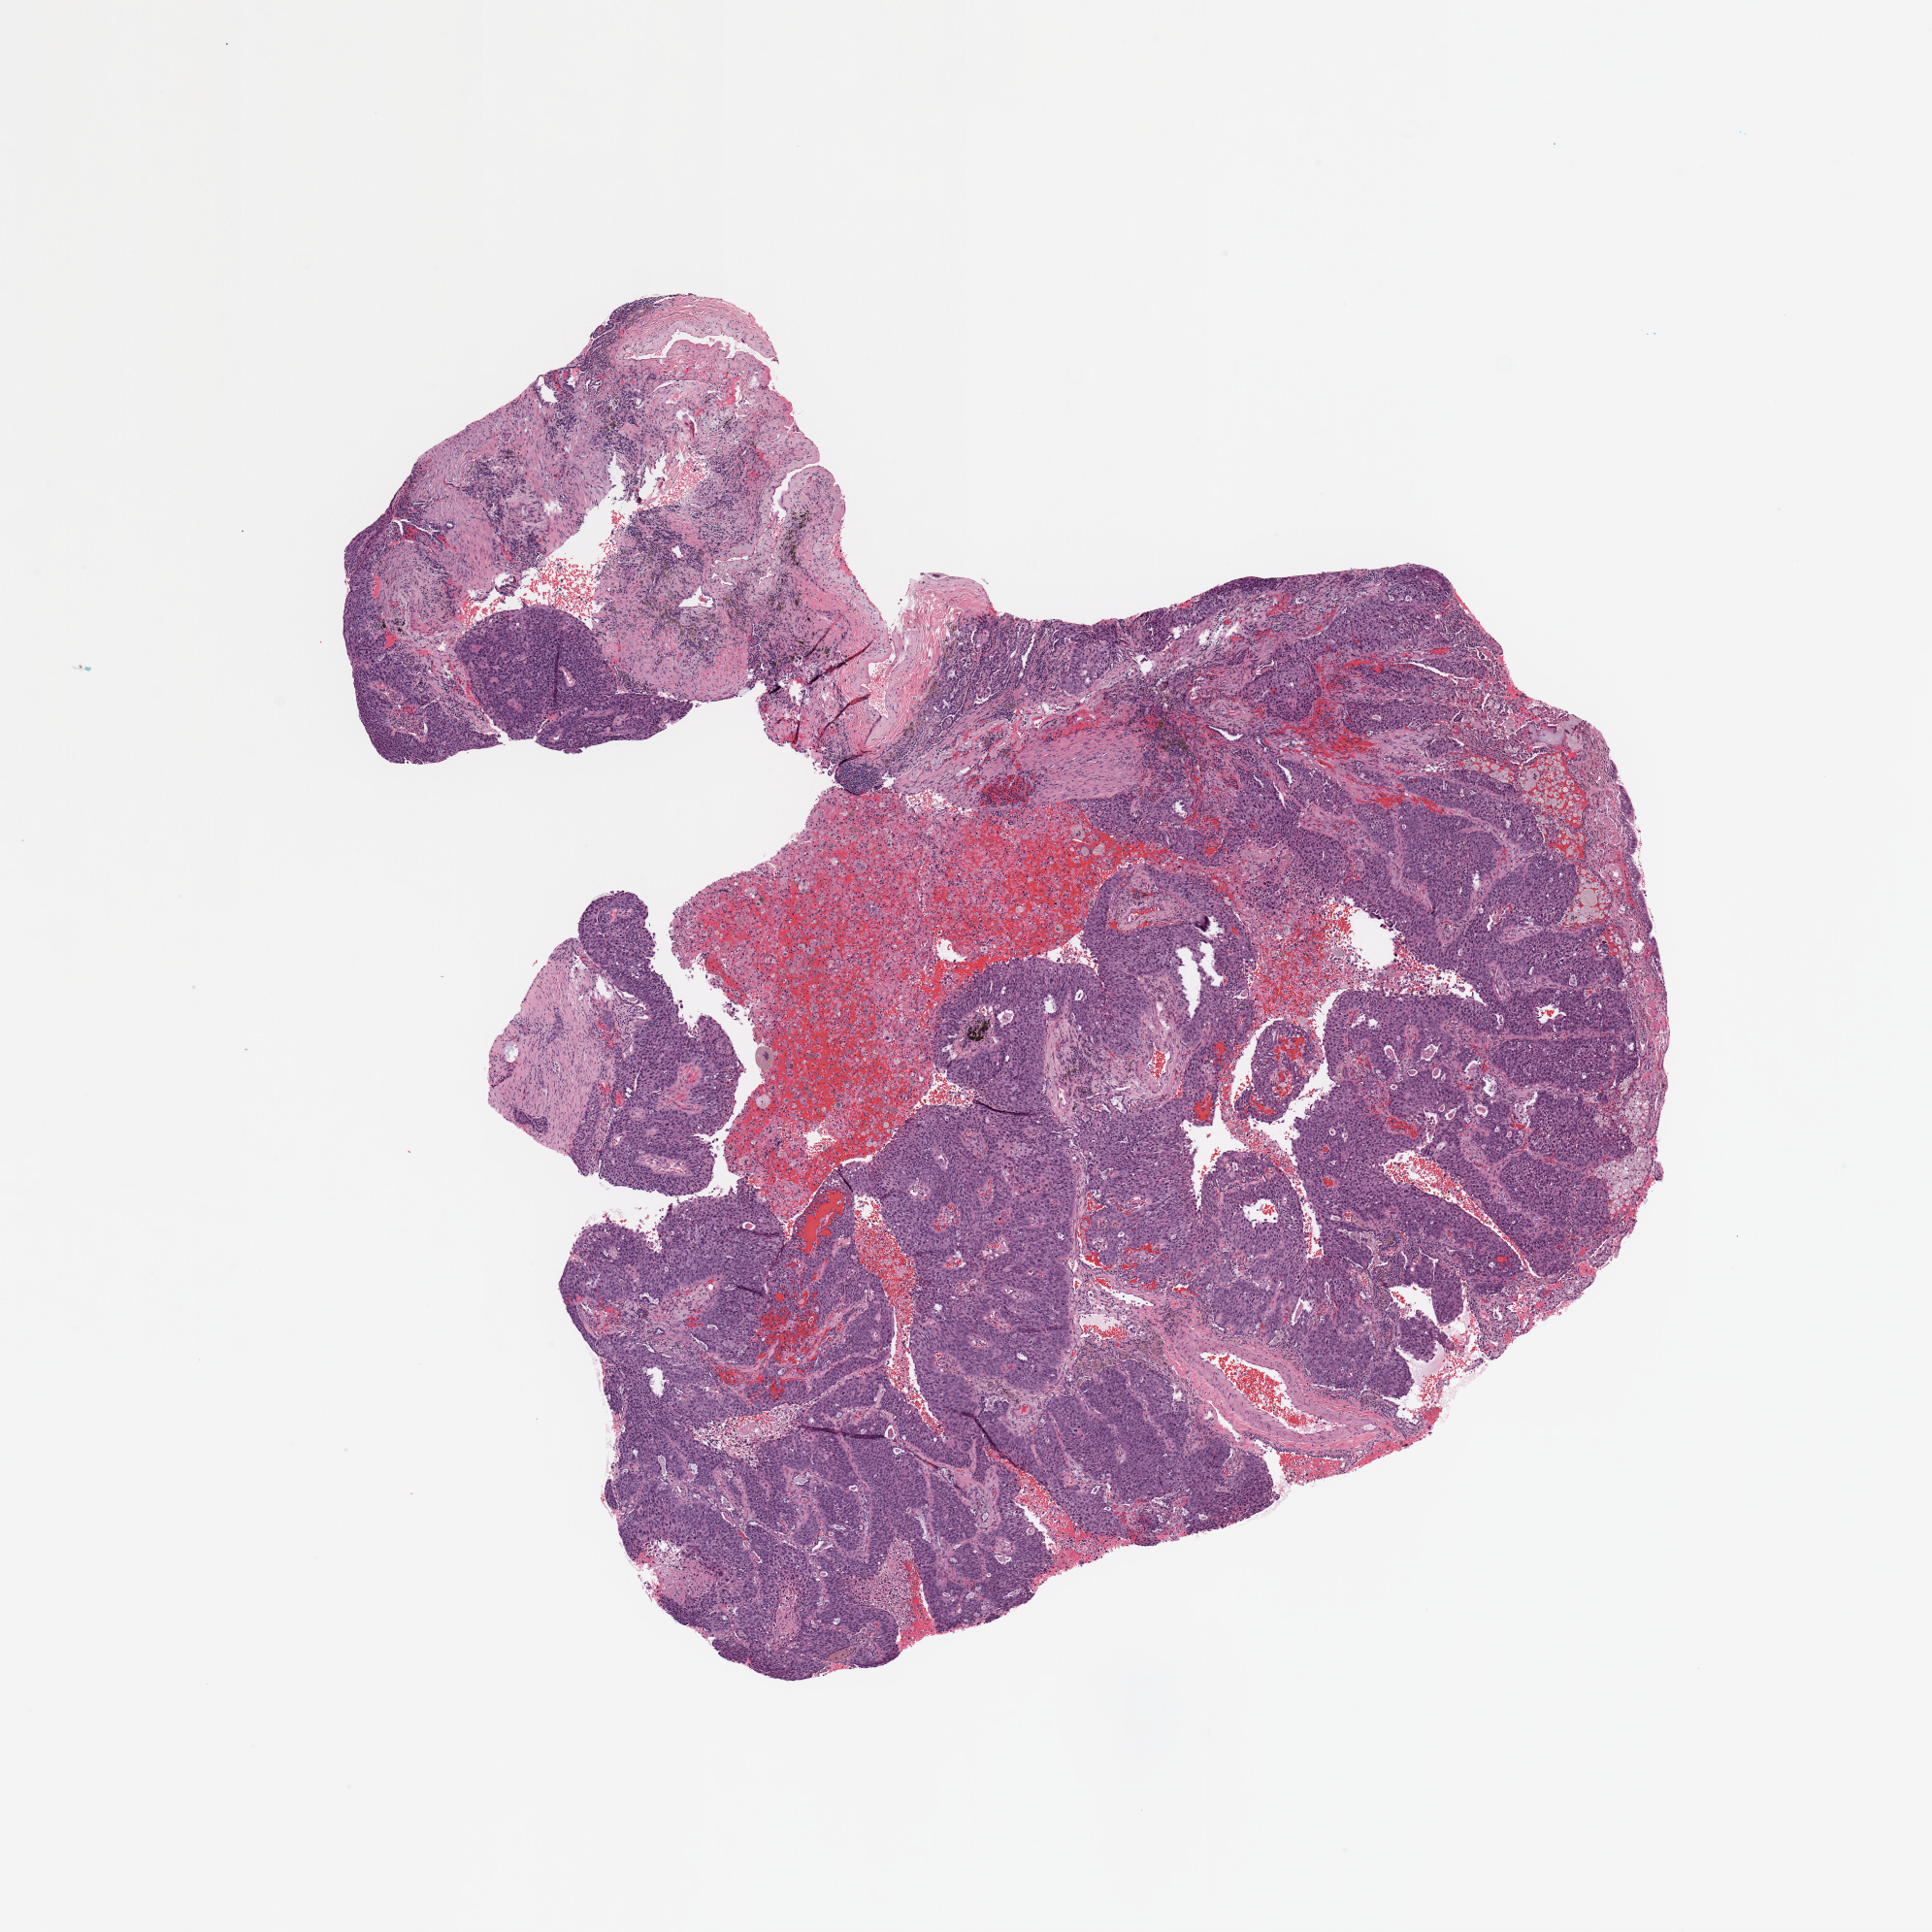
Whole-slide histology image, H&E-stained, low-resolution overview of the scanned area, about 7.9 x 7.9 mm. Normal (non-tumour) tissue sample, lung. Patient: male, age 49 years.
This section: normal (non-tumour) tissue from the same patient. Patient diagnosis: Squamous cell carcinoma, NOS.